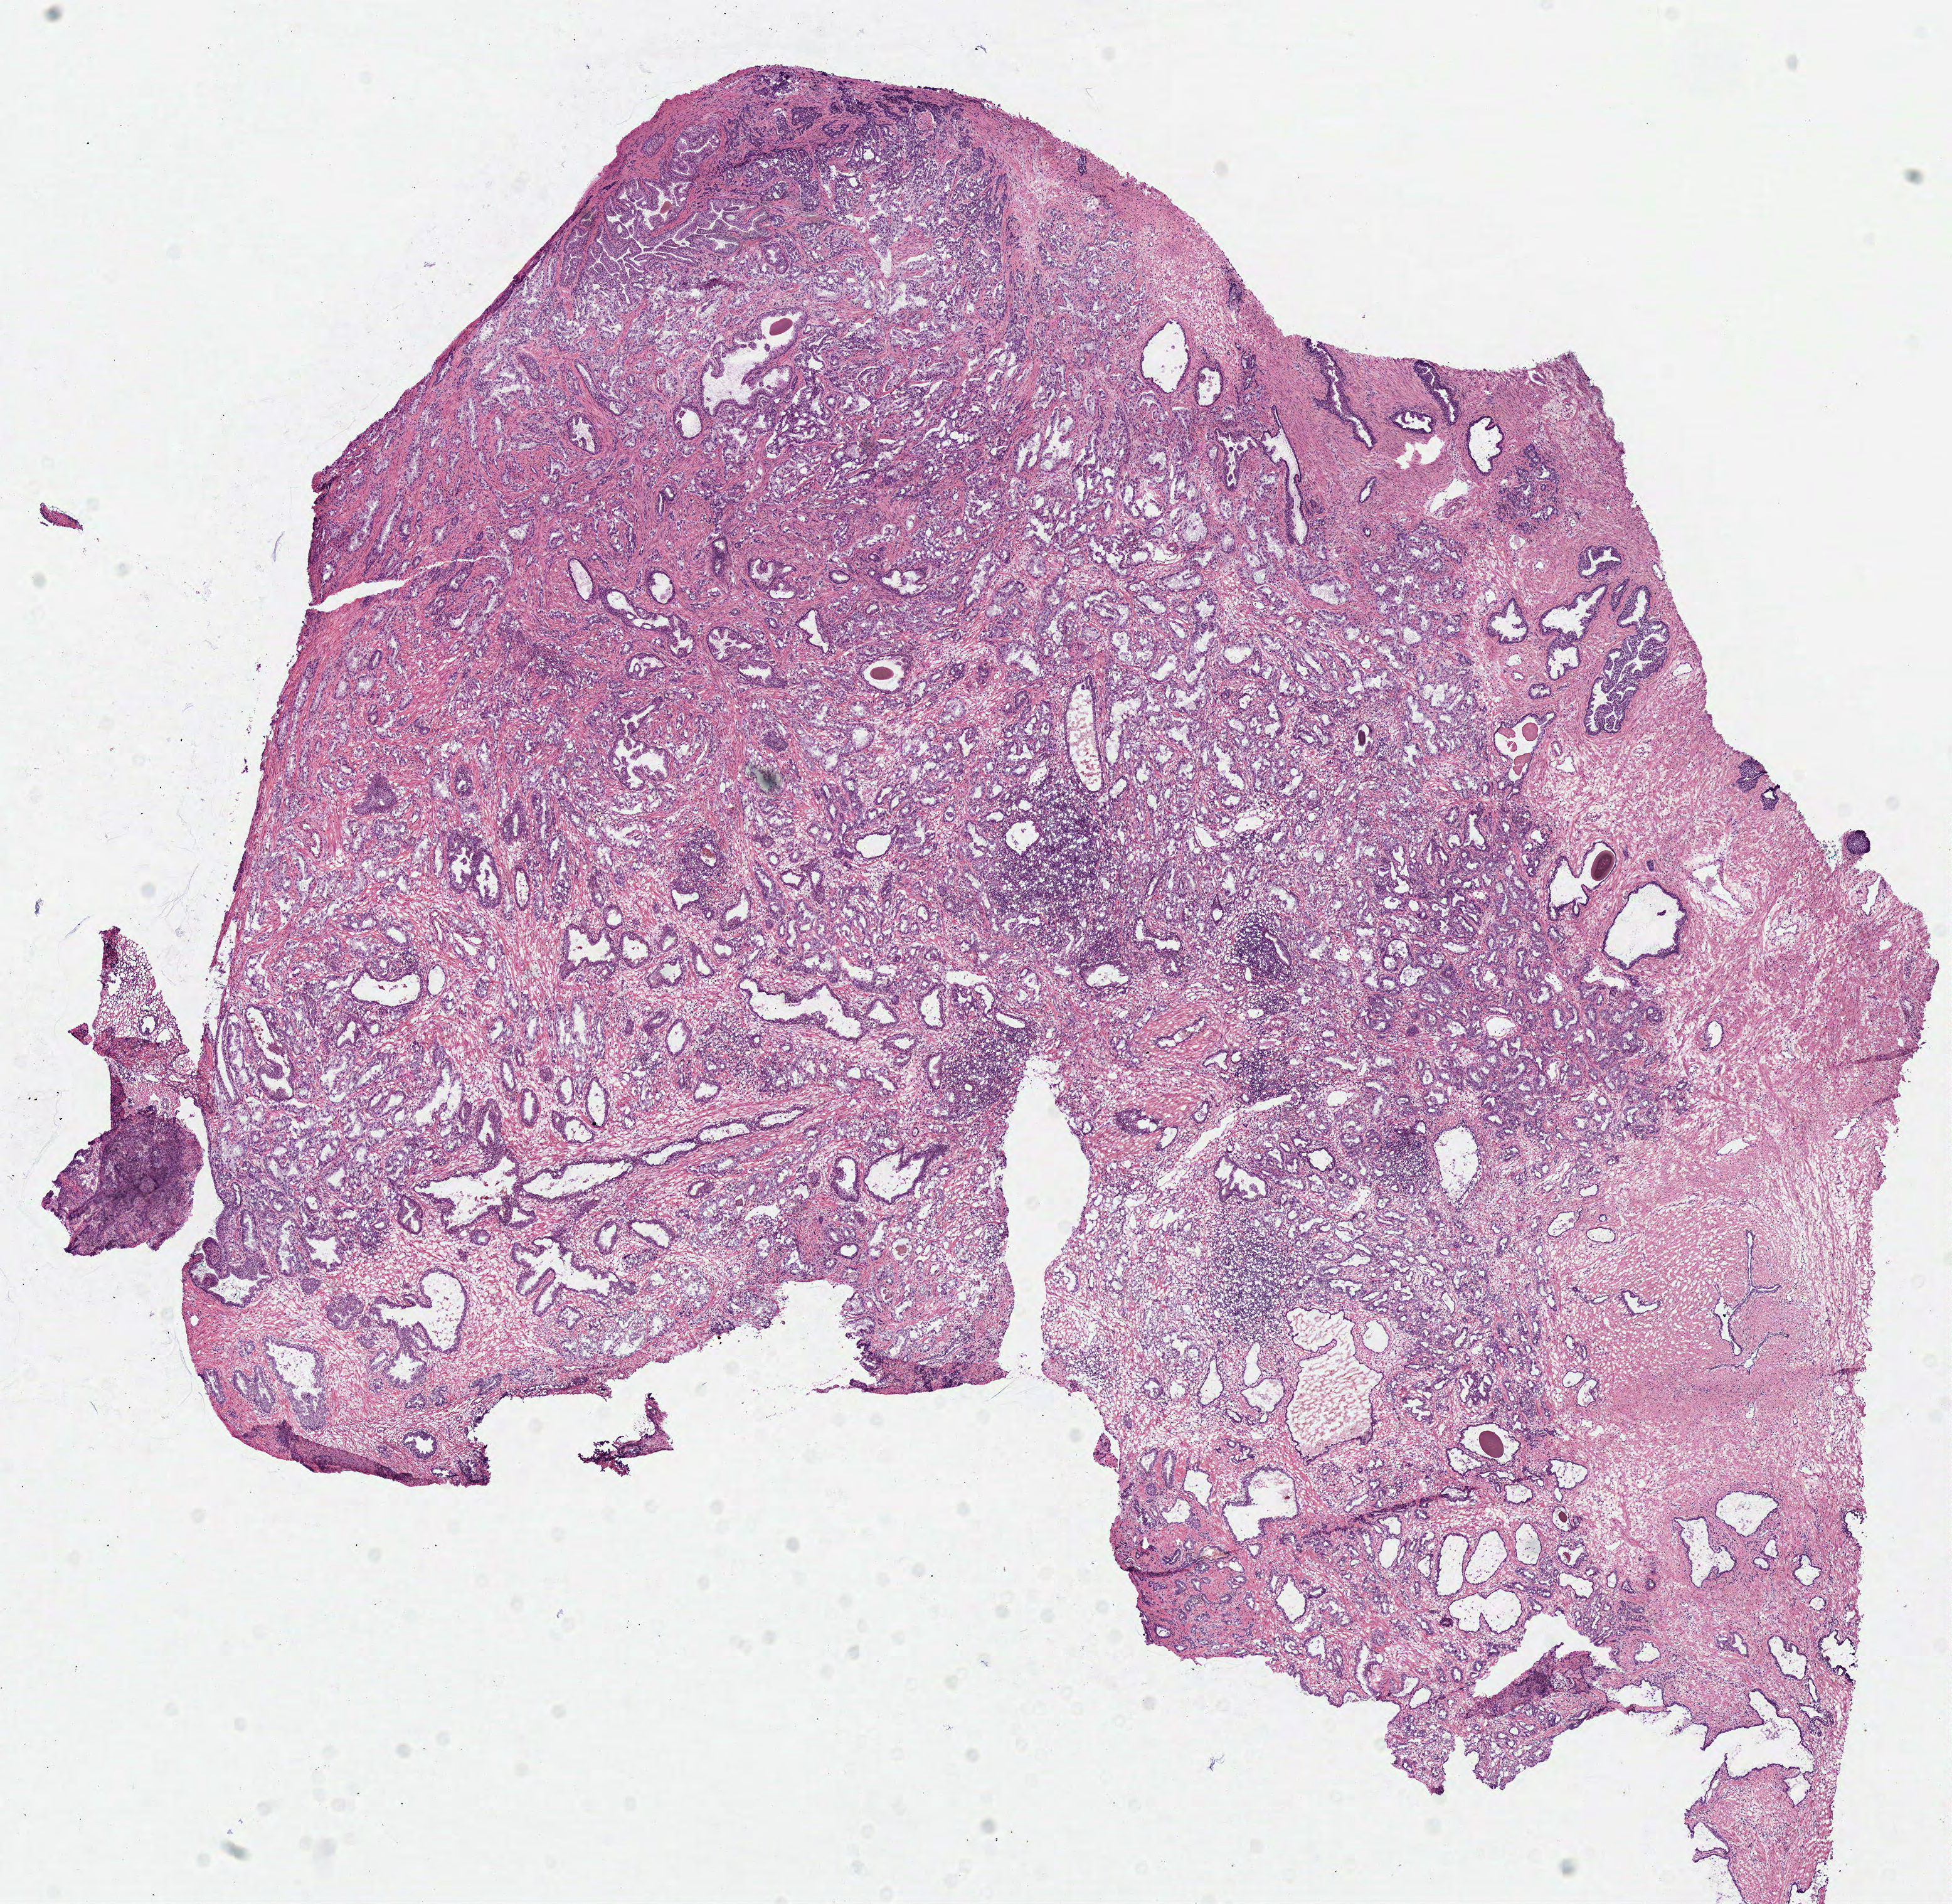
Whole-slide histology image, Hematoxylin and eosin (H&E) stained, a low-resolution overview of the entire scanned area, about 12.2 x 11.9 mm. Frozen section. Prostate, primary tumour sample. Male patient; age at initial diagnosis 68 years. Gleason score: 7 (4+3). Slide review estimates, as recorded: tumour cells 50%, tumour nuclei 70%, normal cells 30%, stromal cells 20%, necrosis 0%. Inflammatory infiltration, as recorded: lymphocyte infiltration 1%, monocyte infiltration 1%, neutrophil infiltration 0%.
- pathologic diagnosis: Acinar cell carcinoma (prostate gland)
- lymph nodes positive (case pathology): 0 of 6 examined
- laterality: bilateral